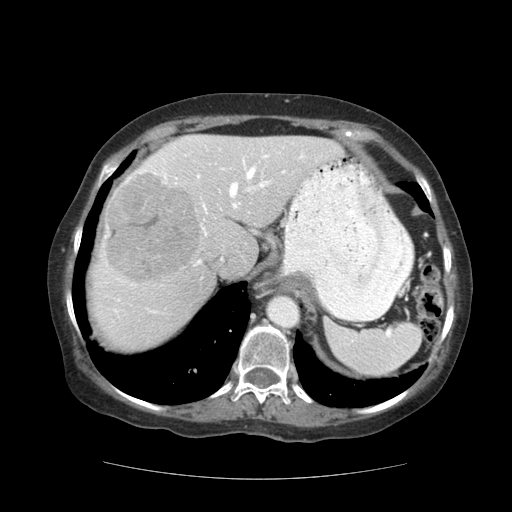
Contrast-enhanced abdominal CT (liver protocol), one axial slice. Position 87 of 111 along the scan axis. 140 kVp. Soft-tissue window (W 400 / L 40 HU). 512 × 512 image matrix. From the clinical record (not read from this slice): diagnosis: hepatocellular carcinoma (patient treated with transarterial chemoembolisation; whether this scan precedes or follows treatment is not stated here); TNM stage (as recorded): Stage-I; Child-Pugh class: A.
Structures marked on this image (semi-automatic segmentation, software-assisted and operator-edited):
- liver parenchyma outside the tumour (the mass and vessels are separate outlines, so this box may not span the whole liver): bounding box [x1, y1, x2, y2] px = [90, 134, 342, 350]
- mass: [105, 172, 202, 284]
- liver vessels: [105, 138, 305, 313]